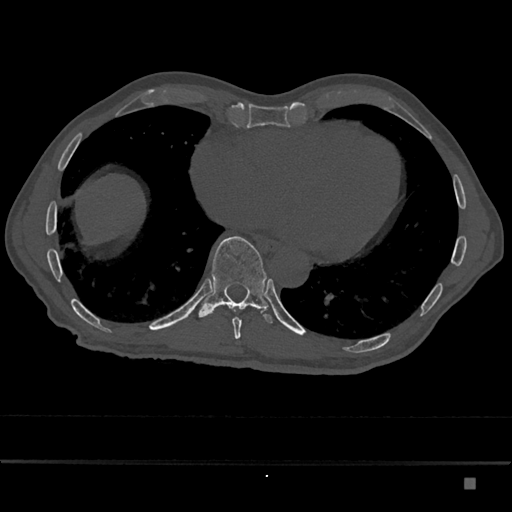
CT including the spine, one axial slice. Slice 763 of 797 in the series (ordered by position). Reconstruction kernel Br40s/3. 120 kVp. Bone window (W 1800 / L 400 HU). 512 × 512 image matrix, field of view 390 × 390 mm. Patient: male, 72 years. Case-level facts recorded for this patient, not image findings: primary cancer: prostate.
Outlined on this slice (semi-automatically segmented with operator editing):
- T10 vertebra: box from (x=198, y=236) to (x=273, y=323) px
- T9 vertebra: (x=232, y=309)–(x=244, y=339)